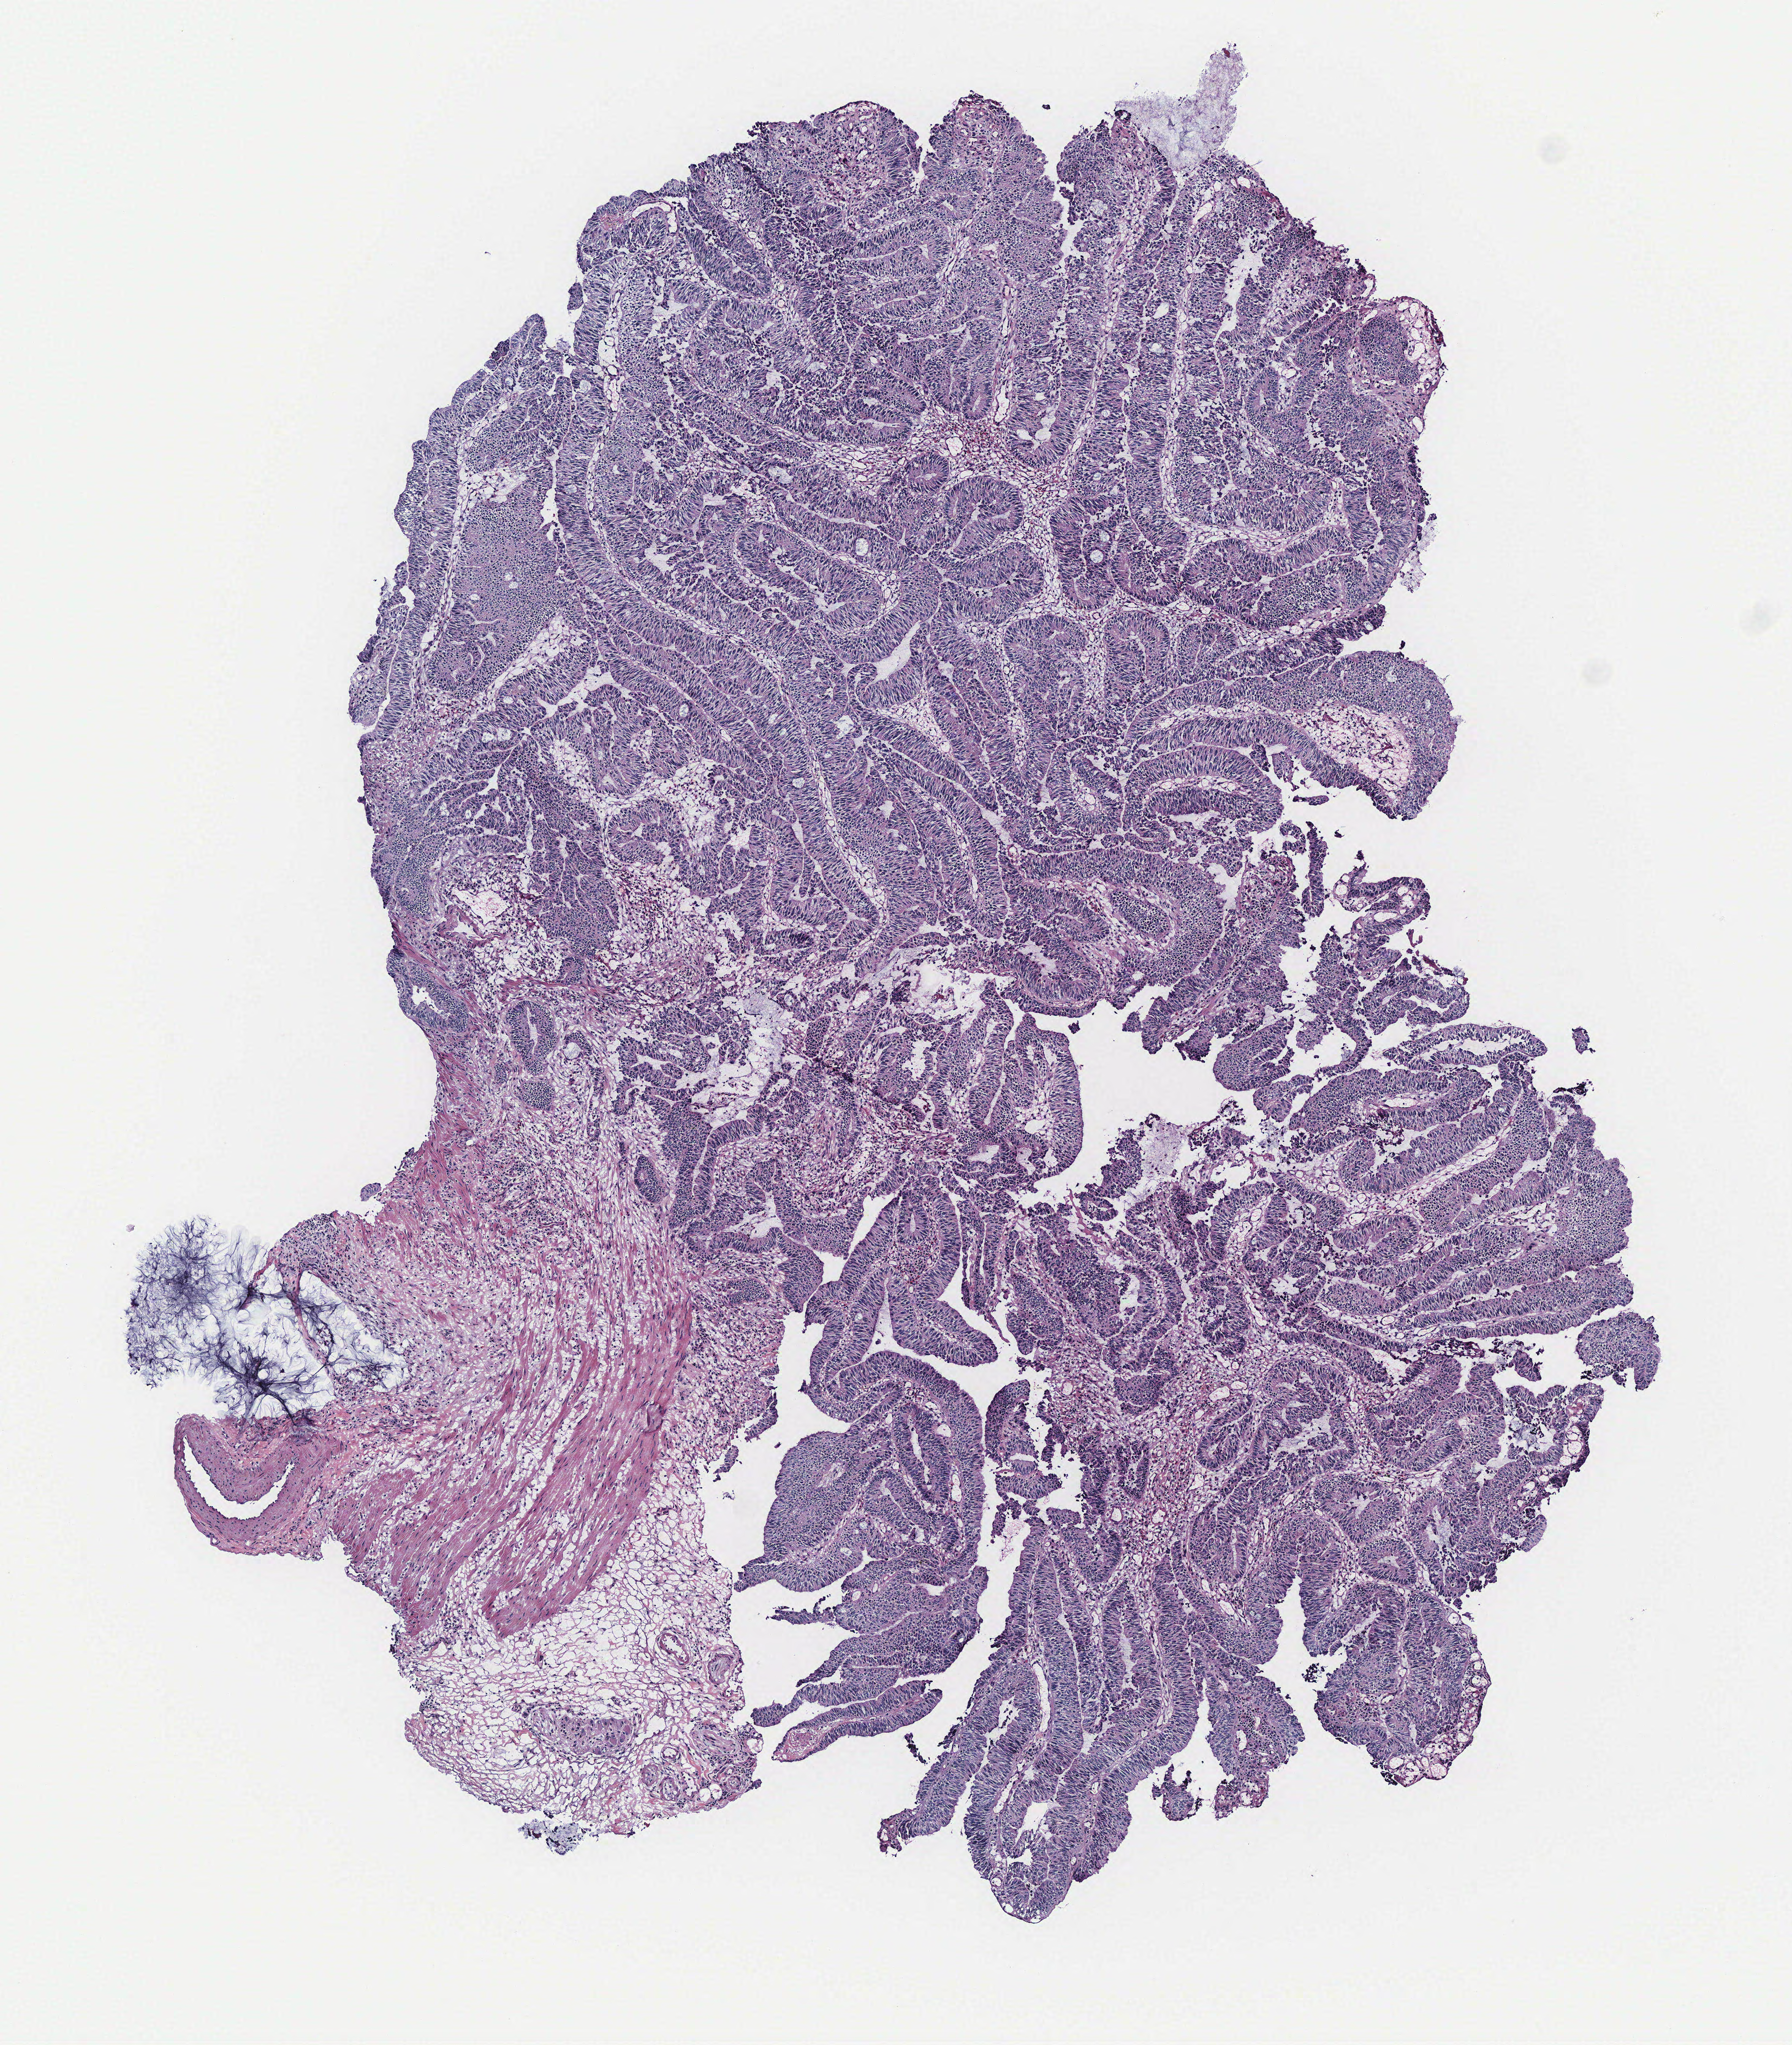
Digitized Hematoxylin and eosin (H&E) stained tissue section (whole slide), low-resolution overview of the scanned area, about 5.3 x 6.0 mm (from a 40x scan); colon, tissue type not recorded.
- patient diagnosis (cohort enrolment): colon cancer (colon)